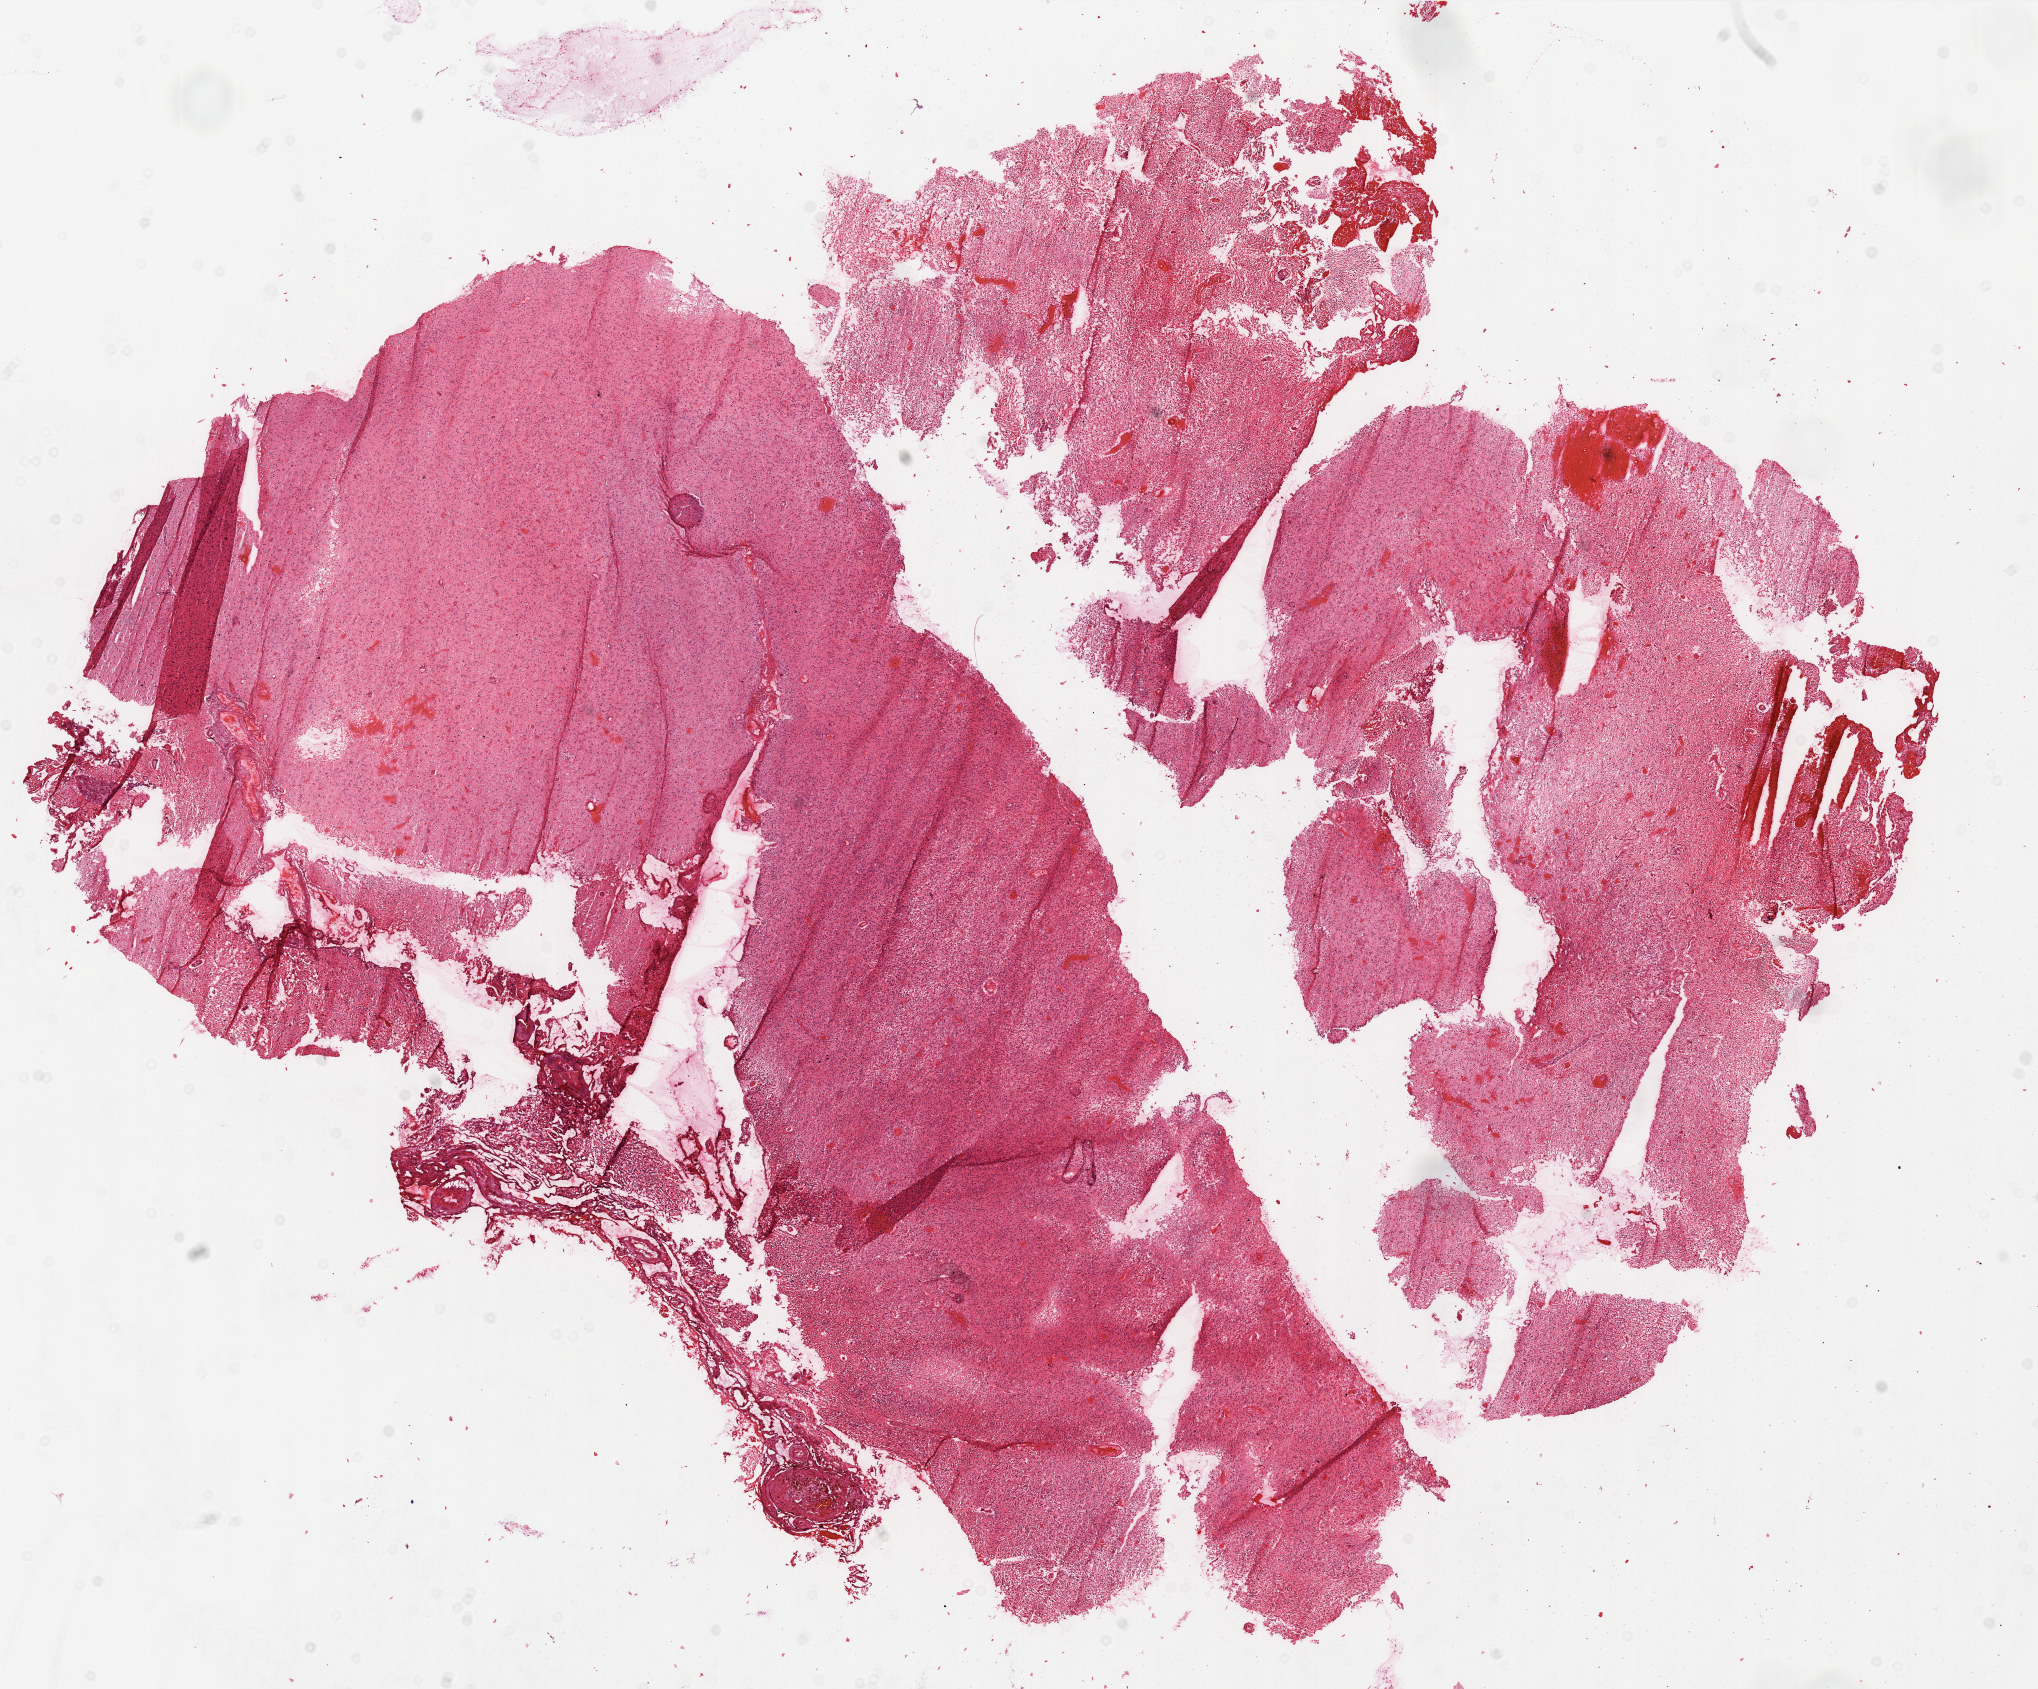
Whole-slide histology image, H&E-stained, a low-resolution overview of the entire scanned area, about 16.4 x 13.6 mm. FFPE section. Primary tumour sample from the brain. Female, age 38 years at initial diagnosis.
Histologic diagnosis: Glioblastoma.